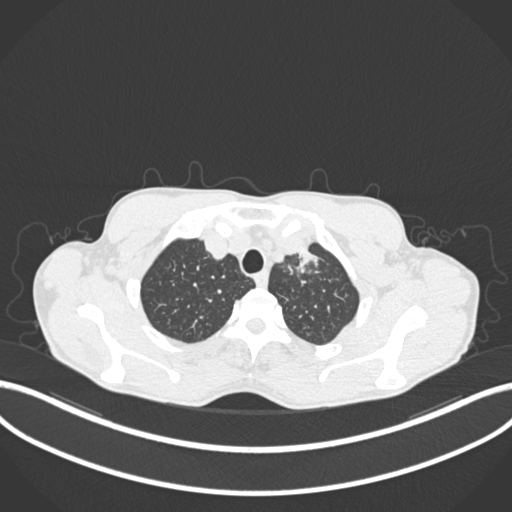
Chest CT, one axial slice; position 179 of 211 along the scan axis; reconstruction kernel B30f; 120 kVp; lung window (W 1500 / L -600 HU); 512 × 512 image matrix. Patient: male, 58 years. Case-level facts recorded for this patient, not image findings: clinical TNM (as recorded): T1c N1 M0.
Annotated regions visible in this slice (bounding box drawn by a radiologist):
- lung tumour (recorded histology: adenocarcinoma): bounding box <290,241,323,280> (left, top, right, bottom; pixels)